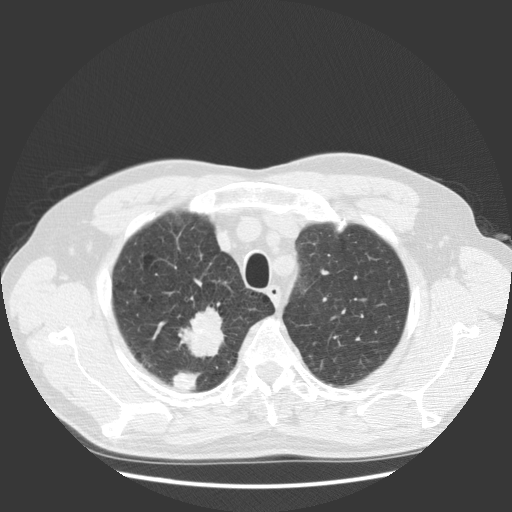
Chest CT (low-dose screening protocol), one axial image. First (baseline) screen. Lung window (W 1500 / L -600 HU). 2.5 mm slice thickness. 140 kVp. Slice 105 of 131 in the series. Male participant, aged 63 years at enrolment. Current smoker at enrolment.
Expert-annotated lung lesion, bounding box [x1, y1, x2, y2] px = [164, 314, 236, 381]. The screening reader recorded 2 non-calcified nodules or masses ≥4 mm on this exam (right upper lobe, right upper lobe); which of them this box marks is not recorded. Official screen result: positive, change unspecified: nodule(s) >= 4 mm or enlarging nodule(s), mass(es), or other non-specific abnormalities suspicious for lung cancer. Later outcome: lung cancer diagnosed 30 days after this screen — squamous cell carcinoma, NOS, right upper lobe, stage IIIB (AJCC 6th edition), 35 mm at pathology.